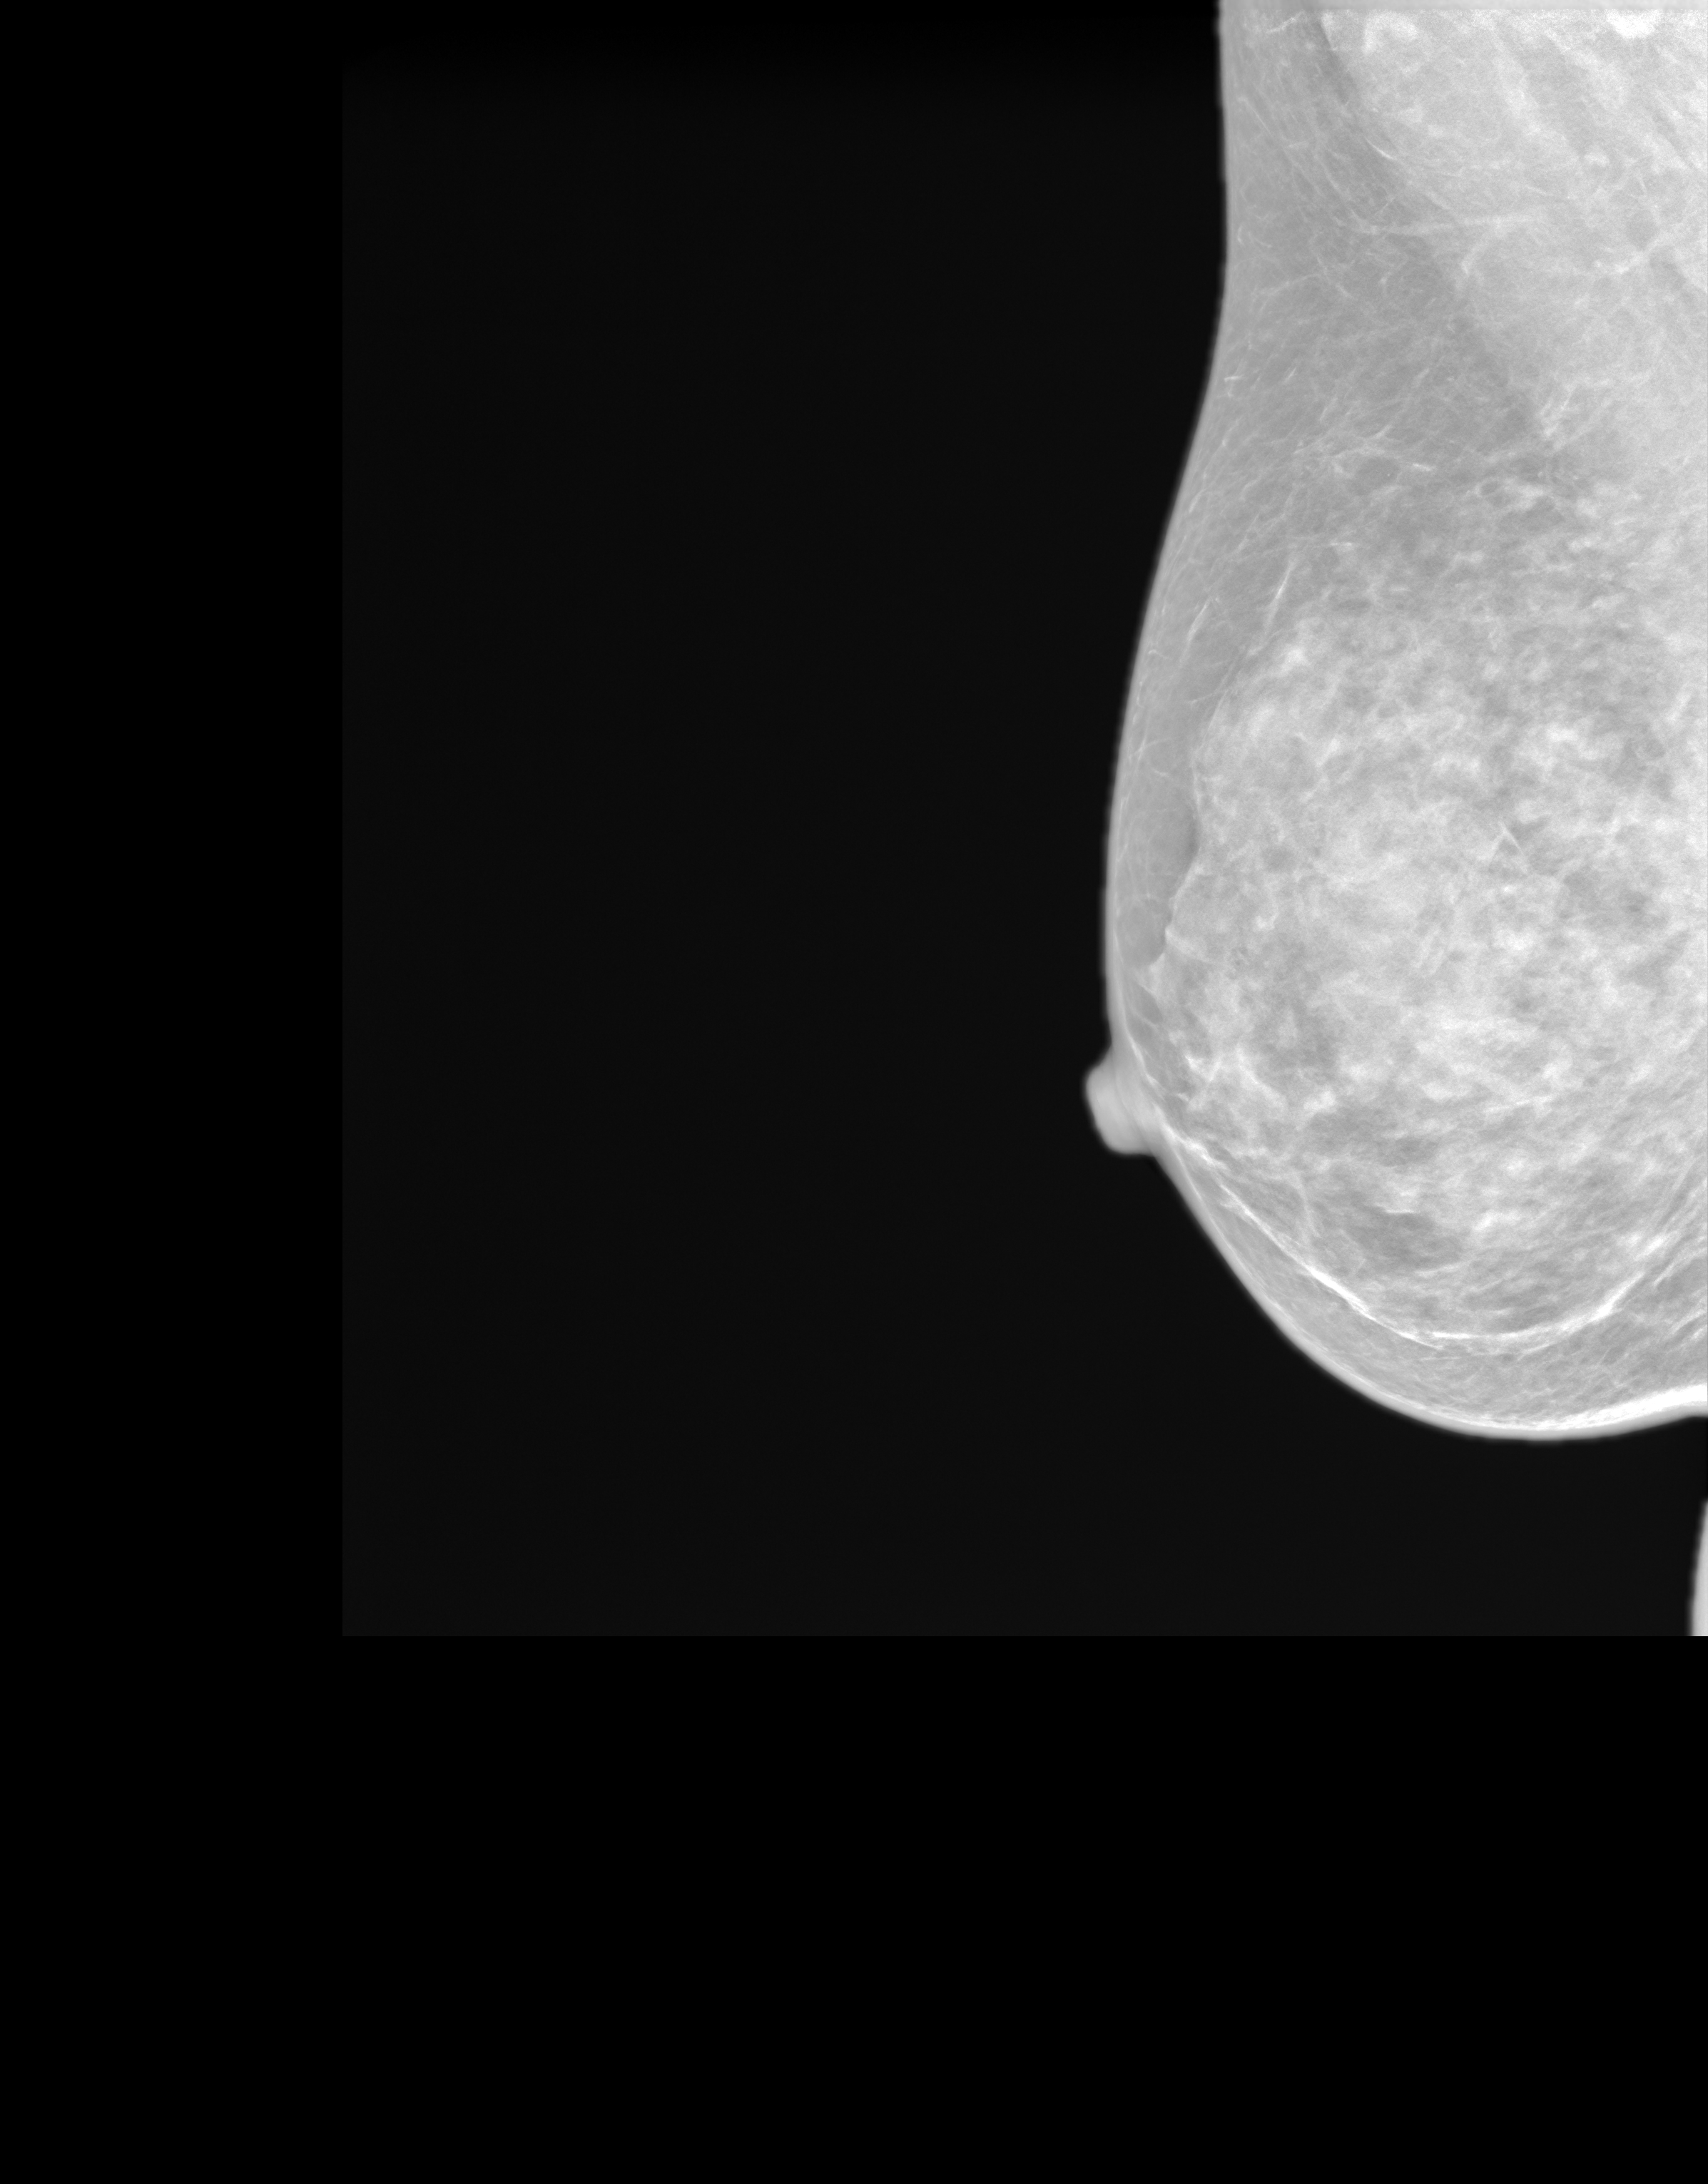
Synthesized 2-D mammogram reconstructed from digital breast tomosynthesis, right breast, MLO view, annual screening mammography examination. Patient aged 60 years (female).
- BI-RADS breast density category at the screening exam (both breasts, scale 1–4): 4
- final BI-RADS assessment for this screening round (tomosynthesis exam, both breasts): category 1
- recall: no recall after this screen